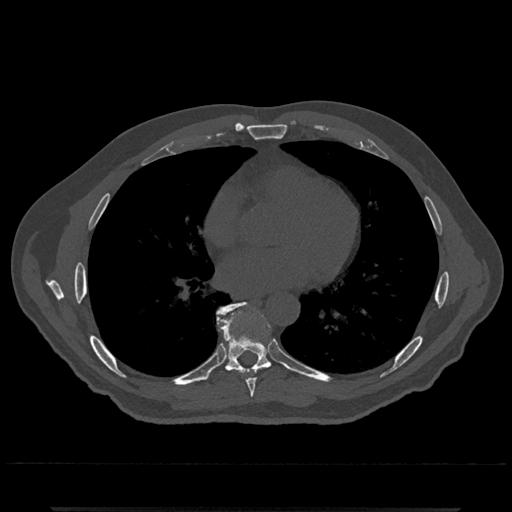
CT including the spine, one axial slice. Position 691 of 797 along the scan axis. Bone window (W 1800 / L 400 HU). 0.5 mm slice thickness. 512 × 512 image matrix. Male patient, age 67 years. Case-level facts recorded for this patient, not image findings: primary cancer: prostate.
Structures marked on this image (semi-automatic segmentation, software-assisted and operator-edited):
- T7 vertebra: bounding box <247,367,266,397> (left, top, right, bottom; pixels)
- T8 vertebra: <212,302,272,382>